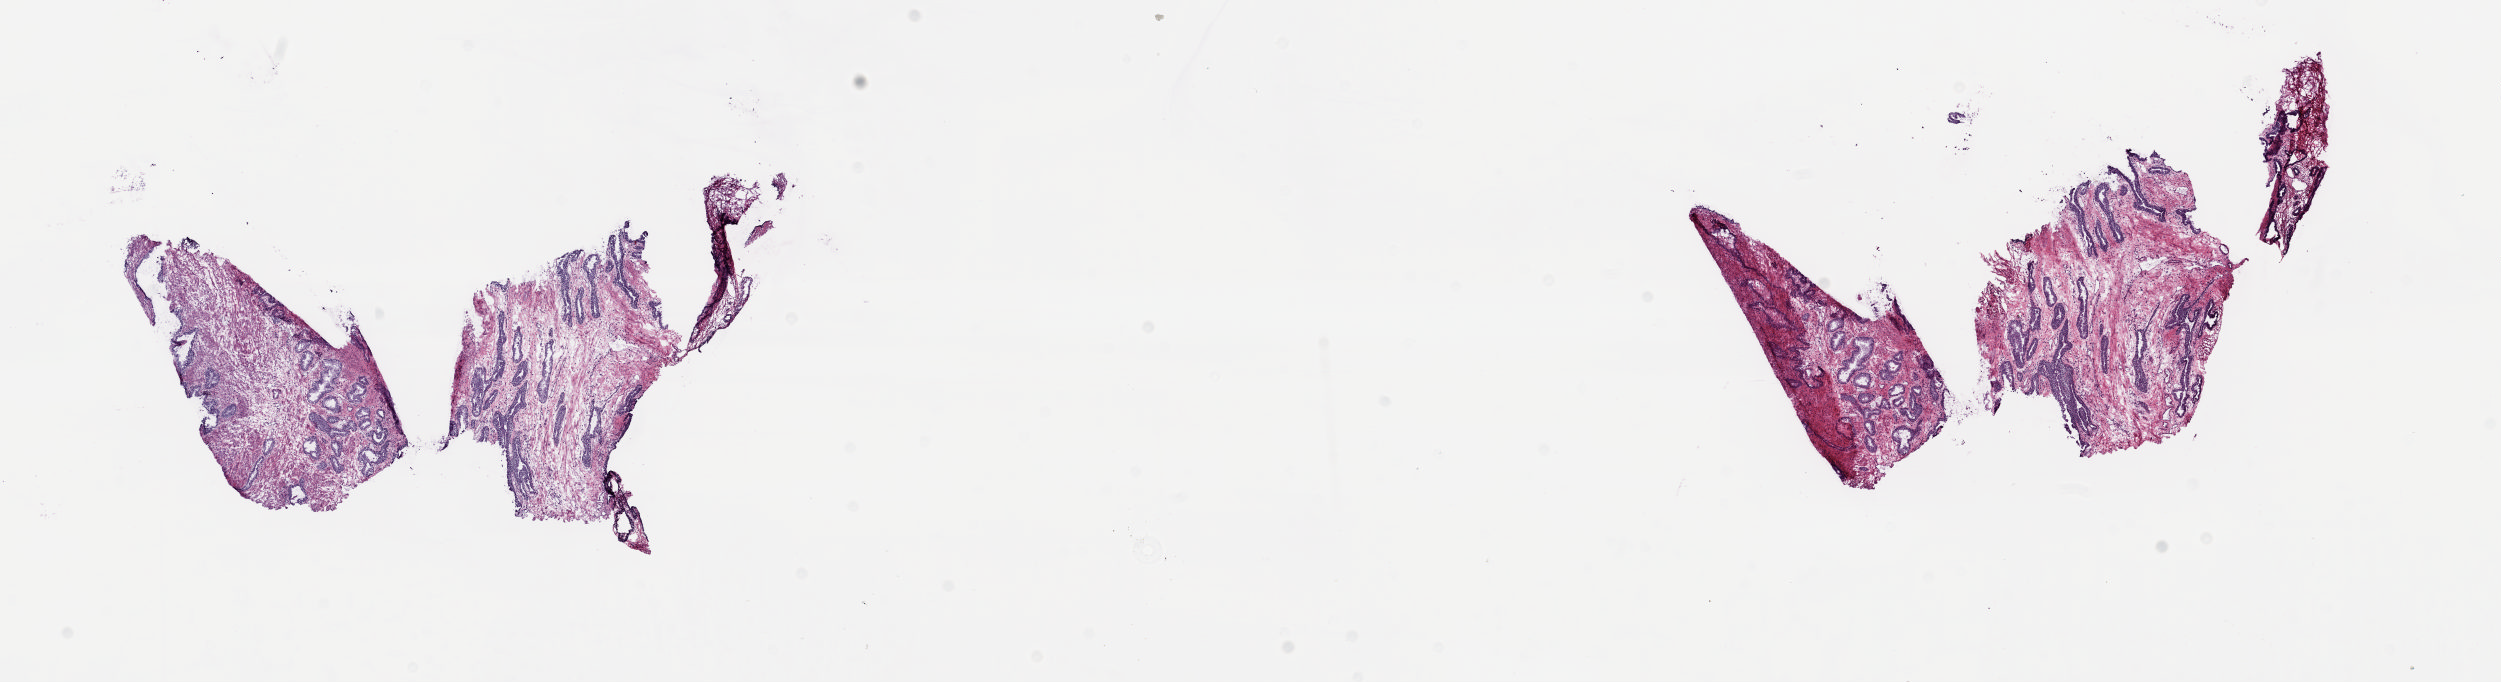
Digitized H&E tissue section (whole slide), low-resolution overview of the scanned area, about 19.8 x 5.4 mm; frozen section from the top of the tissue portion; prostate, solid tissue normal (non-tumour tissue) sample. Patient: male, age at initial diagnosis 68 years. Pathologist review of this section (percent, as recorded): tumour cells 0%, tumour nuclei 0%, normal cells 40%, stromal cells 60%, necrosis 0%. Inflammatory infiltration, as recorded: lymphocyte infiltration 0%, monocyte infiltration 0%, neutrophil infiltration 0%.
This section: solid tissue normal (non-tumour) sample from the same patient. Patient diagnosis: Adenocarcinoma, NOS (prostate gland).